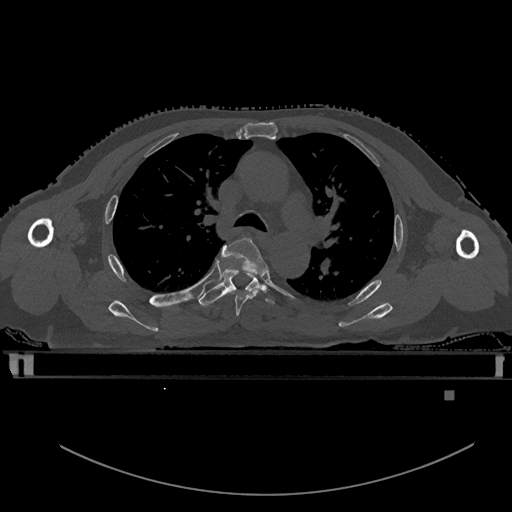
CT including the spine, one axial slice; slice 382 of 969 in the series (ordered by position); bone window (W 1800 / L 400 HU); 512 × 512 image matrix, field of view 456 × 456 mm. Patient: male, 82 years. From the clinical record (not read from this slice): primary cancer: prostate; vertebrae with lytic lesions (as recorded): T11, T9, T8, T2.
Outlined on this slice (semi-automatic segmentation, software-assisted and operator-edited):
- T4 vertebra: box from (x=221, y=237) to (x=268, y=317) px
- T5 vertebra: (x=199, y=269)–(x=275, y=307)